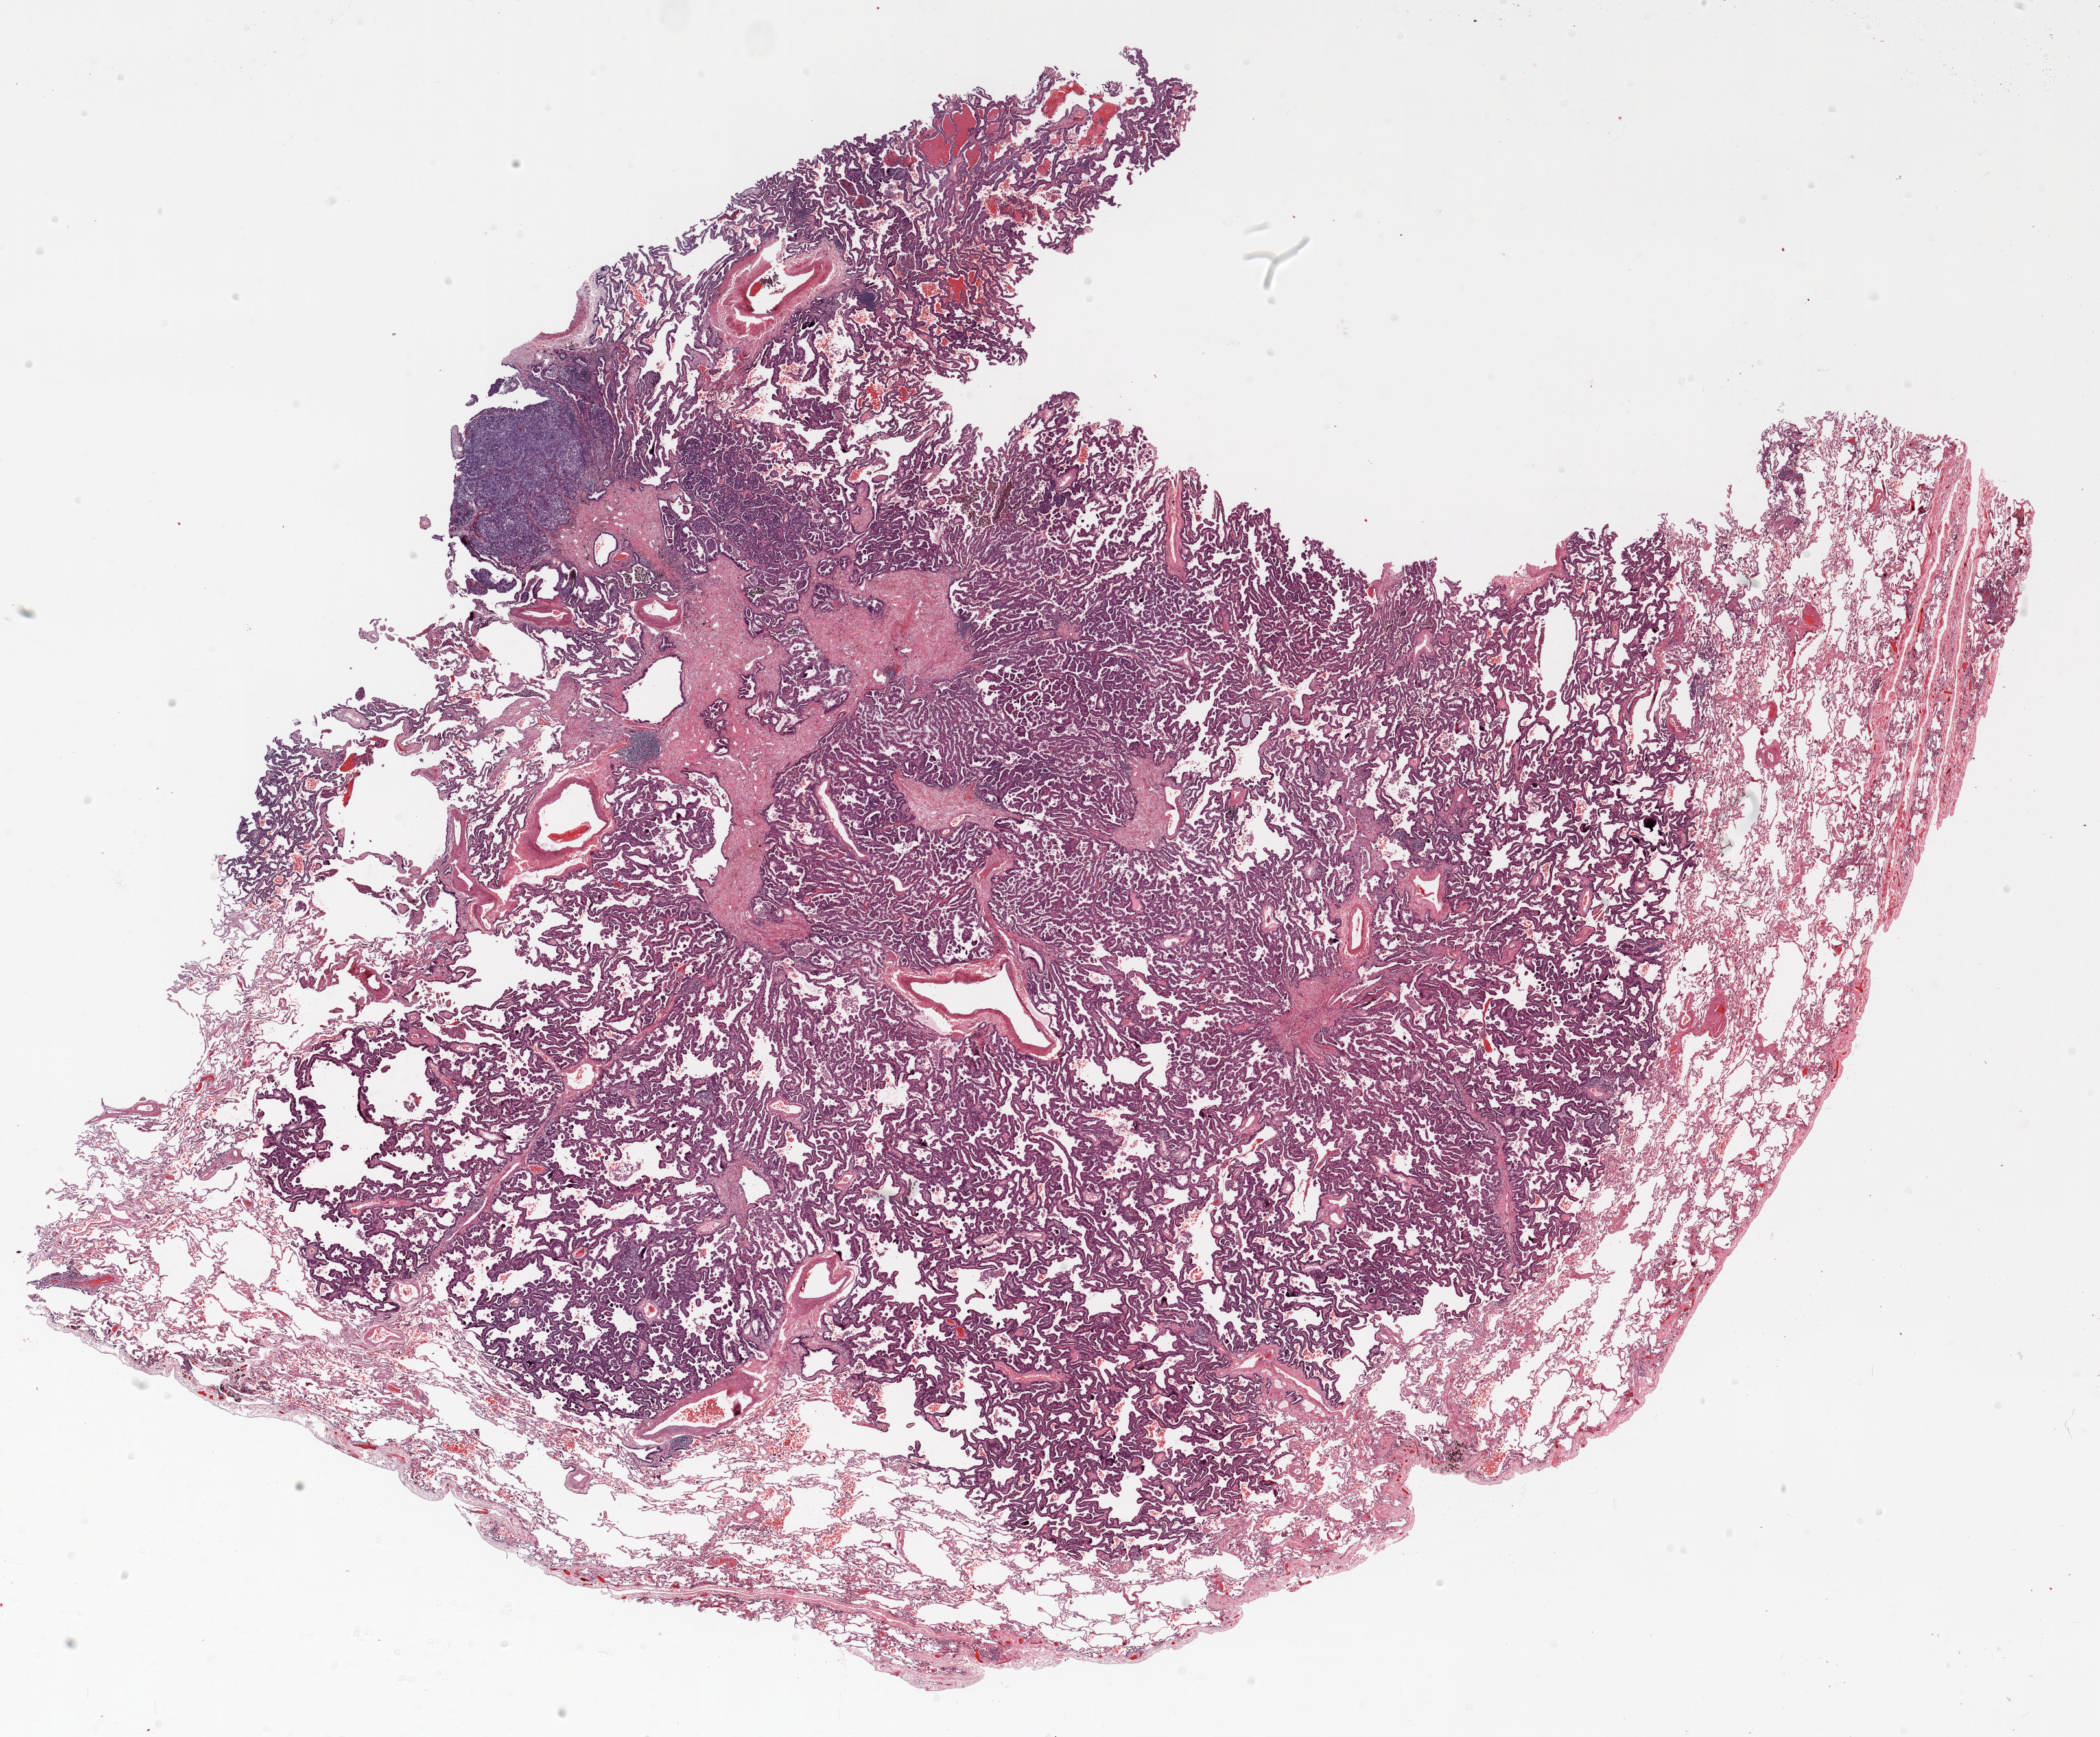
Whole-slide histology image, H&E — whole scanned area (about 26.0 x 21.5 mm, acquisition: 20x scan) shown as a low-resolution overview, FFPE section, lung. Male patient, aged 59 at enrolment. Former smoker at enrolment. Grade: well differentiated (G1).
Tumour size (pathology): 15 mm. Primary tumour location (clinical record): right upper lobe. Participant's lung-cancer diagnosis: Bronchiolo-alveolar carcinoma, non-mucinous. Stage (AJCC 6th edition): IA.